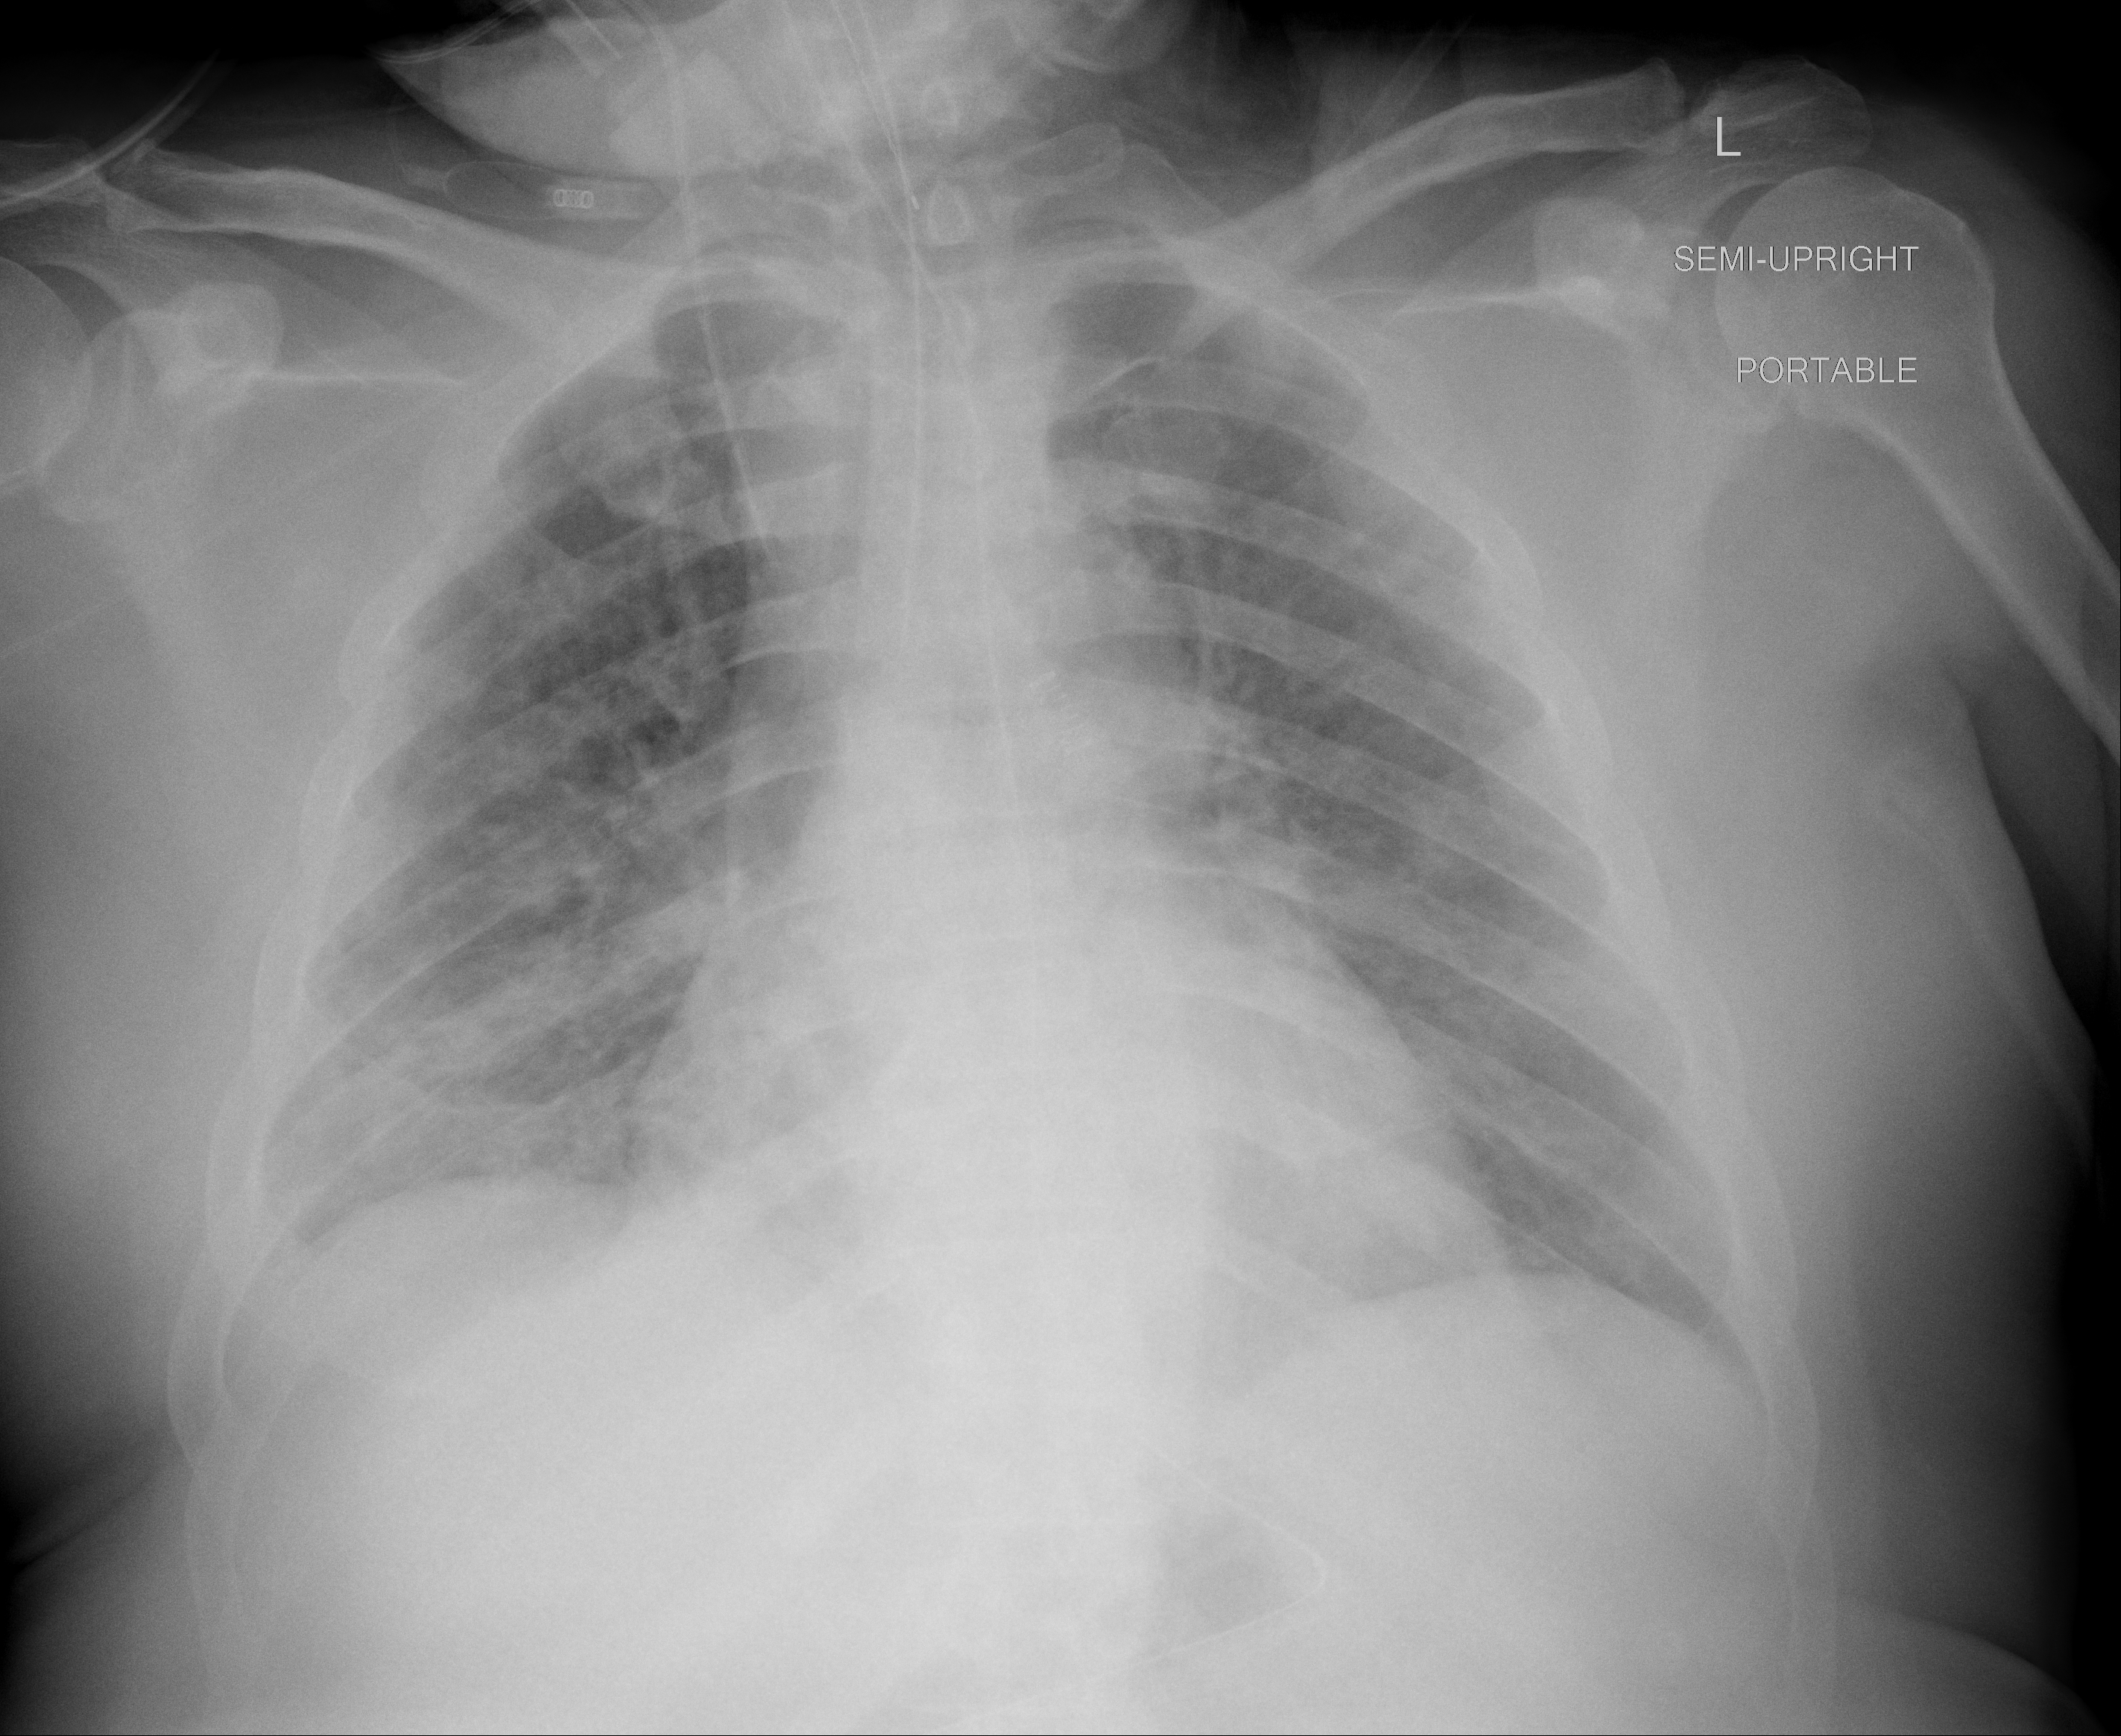
Chest X-ray (portable), AP projection. Male patient, age 55 years; COVID-19 (test-positive).
Key findings recorded by the radiologist: Ill-defined peripheral airspace opacities appear to have improved as compared to the prior study.